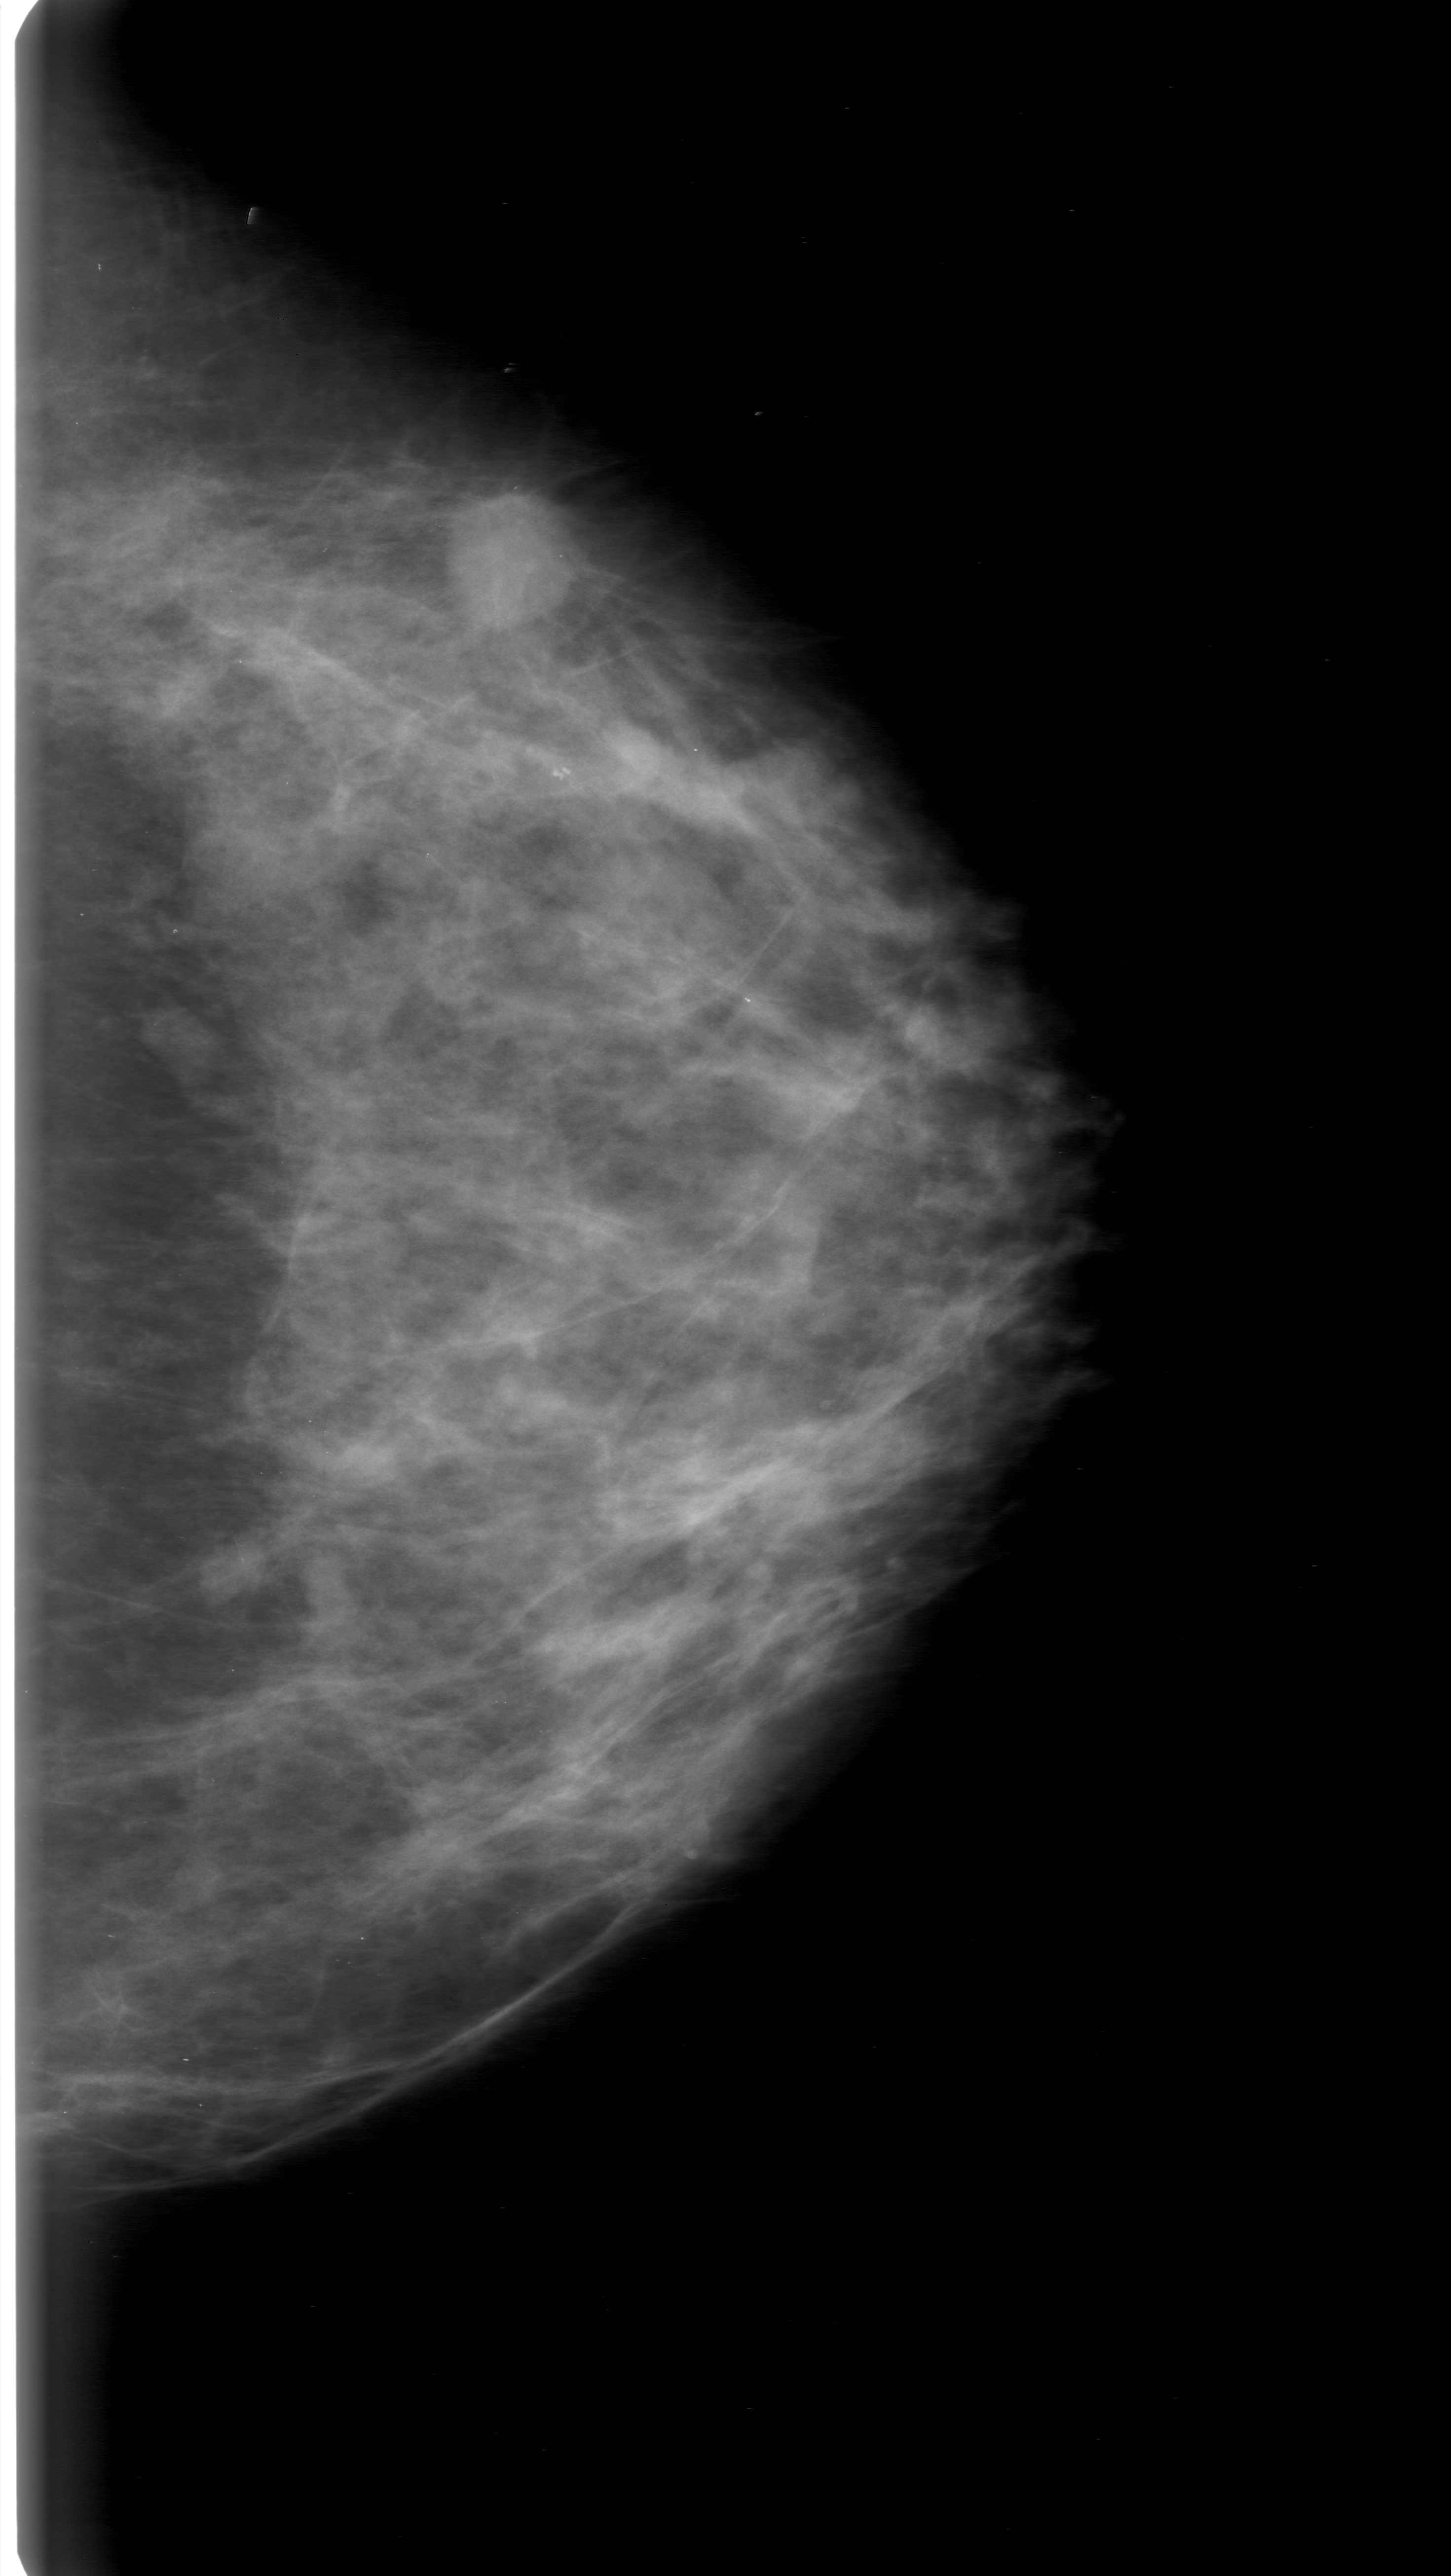
Scanned film-screen mammogram. Left breast. CC view. 1451 × 2576 image matrix.
Expert-marked regions of interest on this film, with their recorded descriptors:
- mass, shape oval, margins microlobulated; BI-RADS assessment category 0; pathology (as recorded): malignant: bounding box [x1, y1, x2, y2] px = [422, 498, 585, 649]